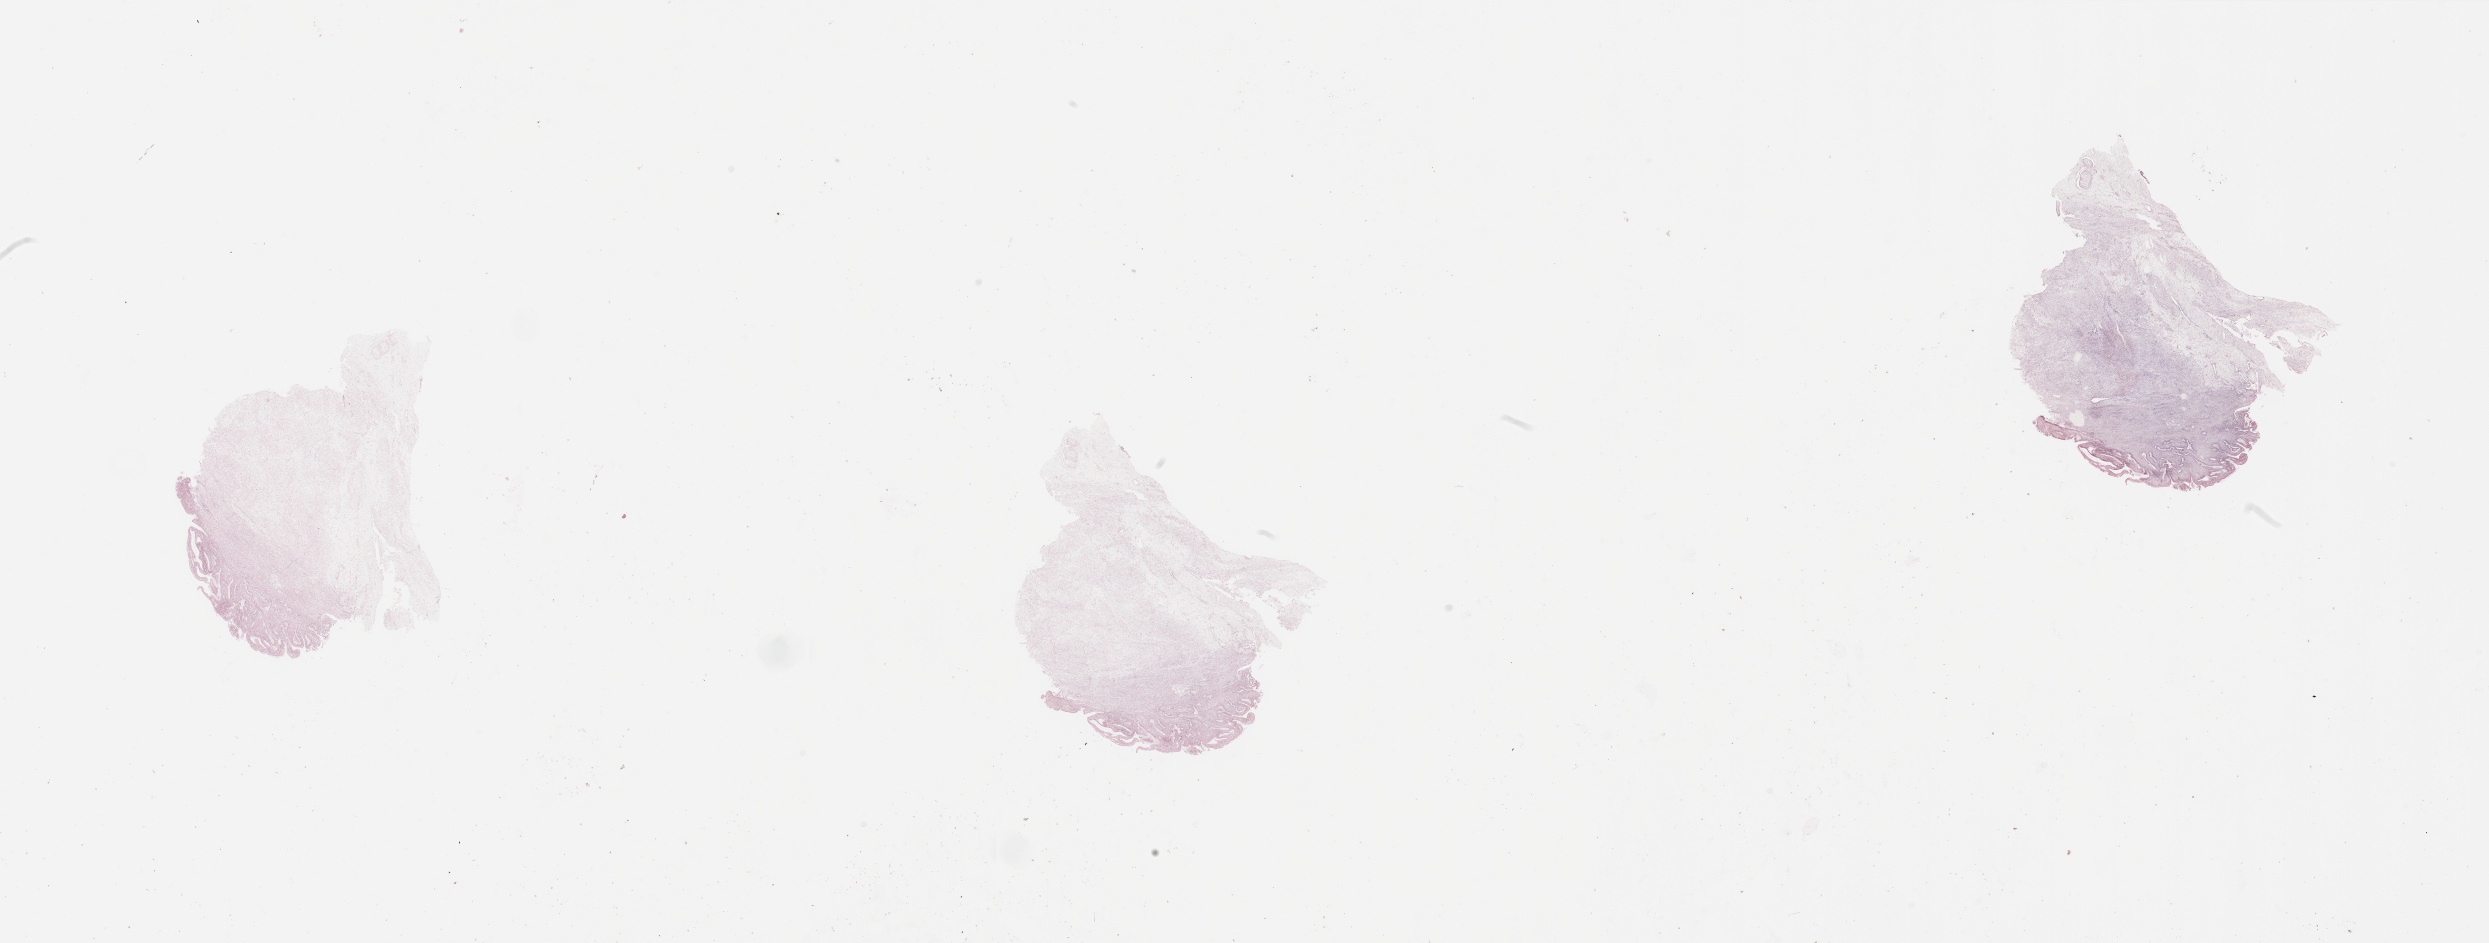
Whole-slide histology image, Hematoxylin and eosin (H&E) stained — low-resolution overview of the scanned area, about 39.4 x 14.9 mm, normal (non-tumour) tissue sample, sampled site: uterus. Female, 75 y/o.
* this section: normal (non-tumour) tissue from the same patient
* patient diagnosis: Endometrioid adenocarcinoma, NOS